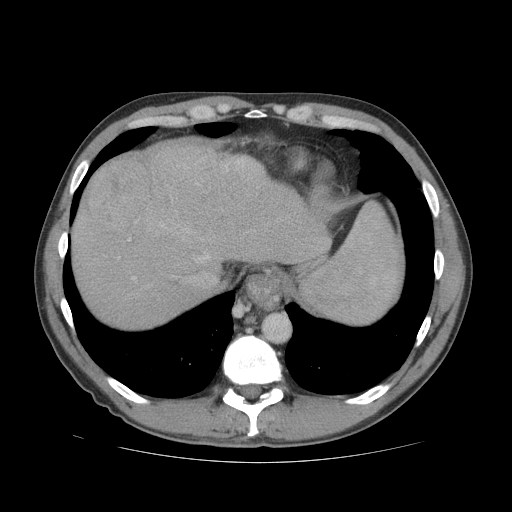
Contrast-enhanced abdominal CT (liver protocol), one axial slice. Slice 63 of 81 in the series (ordered by position). Reconstruction kernel STANDARD. Soft-tissue window (W 400 / L 40 HU). 512 × 512 image matrix. Case-level facts recorded for this patient, not image findings: diagnosis: hepatocellular carcinoma (patient treated with transarterial chemoembolisation; whether this scan precedes or follows treatment is not stated here); TNM stage (as recorded): Stage-IVB; Child-Pugh class: B; tumour differentiation: well differentiated; tumour nodularity: multinodular.
Structures marked on this image (semi-automatic segmentation, software-assisted and operator-edited):
- liver parenchyma outside the tumour (the mass and vessels are separate outlines, so this box may not span the whole liver): bounding box [x1, y1, x2, y2] px = [72, 140, 324, 328]
- mass: [84, 157, 152, 229]
- liver vessels: [129, 160, 245, 279]